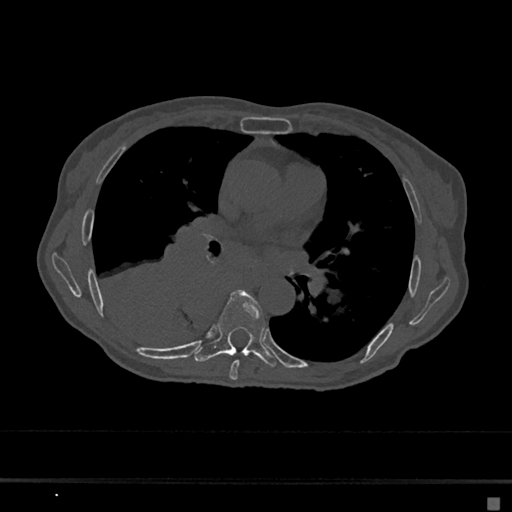
CT including the spine, one axial slice. Position 386 of 797 along the scan axis. 120 kVp. Bone window (W 1800 / L 400 HU). 0.5 mm slice thickness. 512 × 512 image matrix, field of view 360 × 360 mm. Female patient, age 68 years. From the clinical record (not read from this slice): primary cancer: renal.
Annotated regions visible in this slice (semi-automatically segmented with operator editing):
- T6 vertebra: box from (x=229, y=360) to (x=240, y=380) px
- T7 vertebra: (x=194, y=291)–(x=276, y=367)